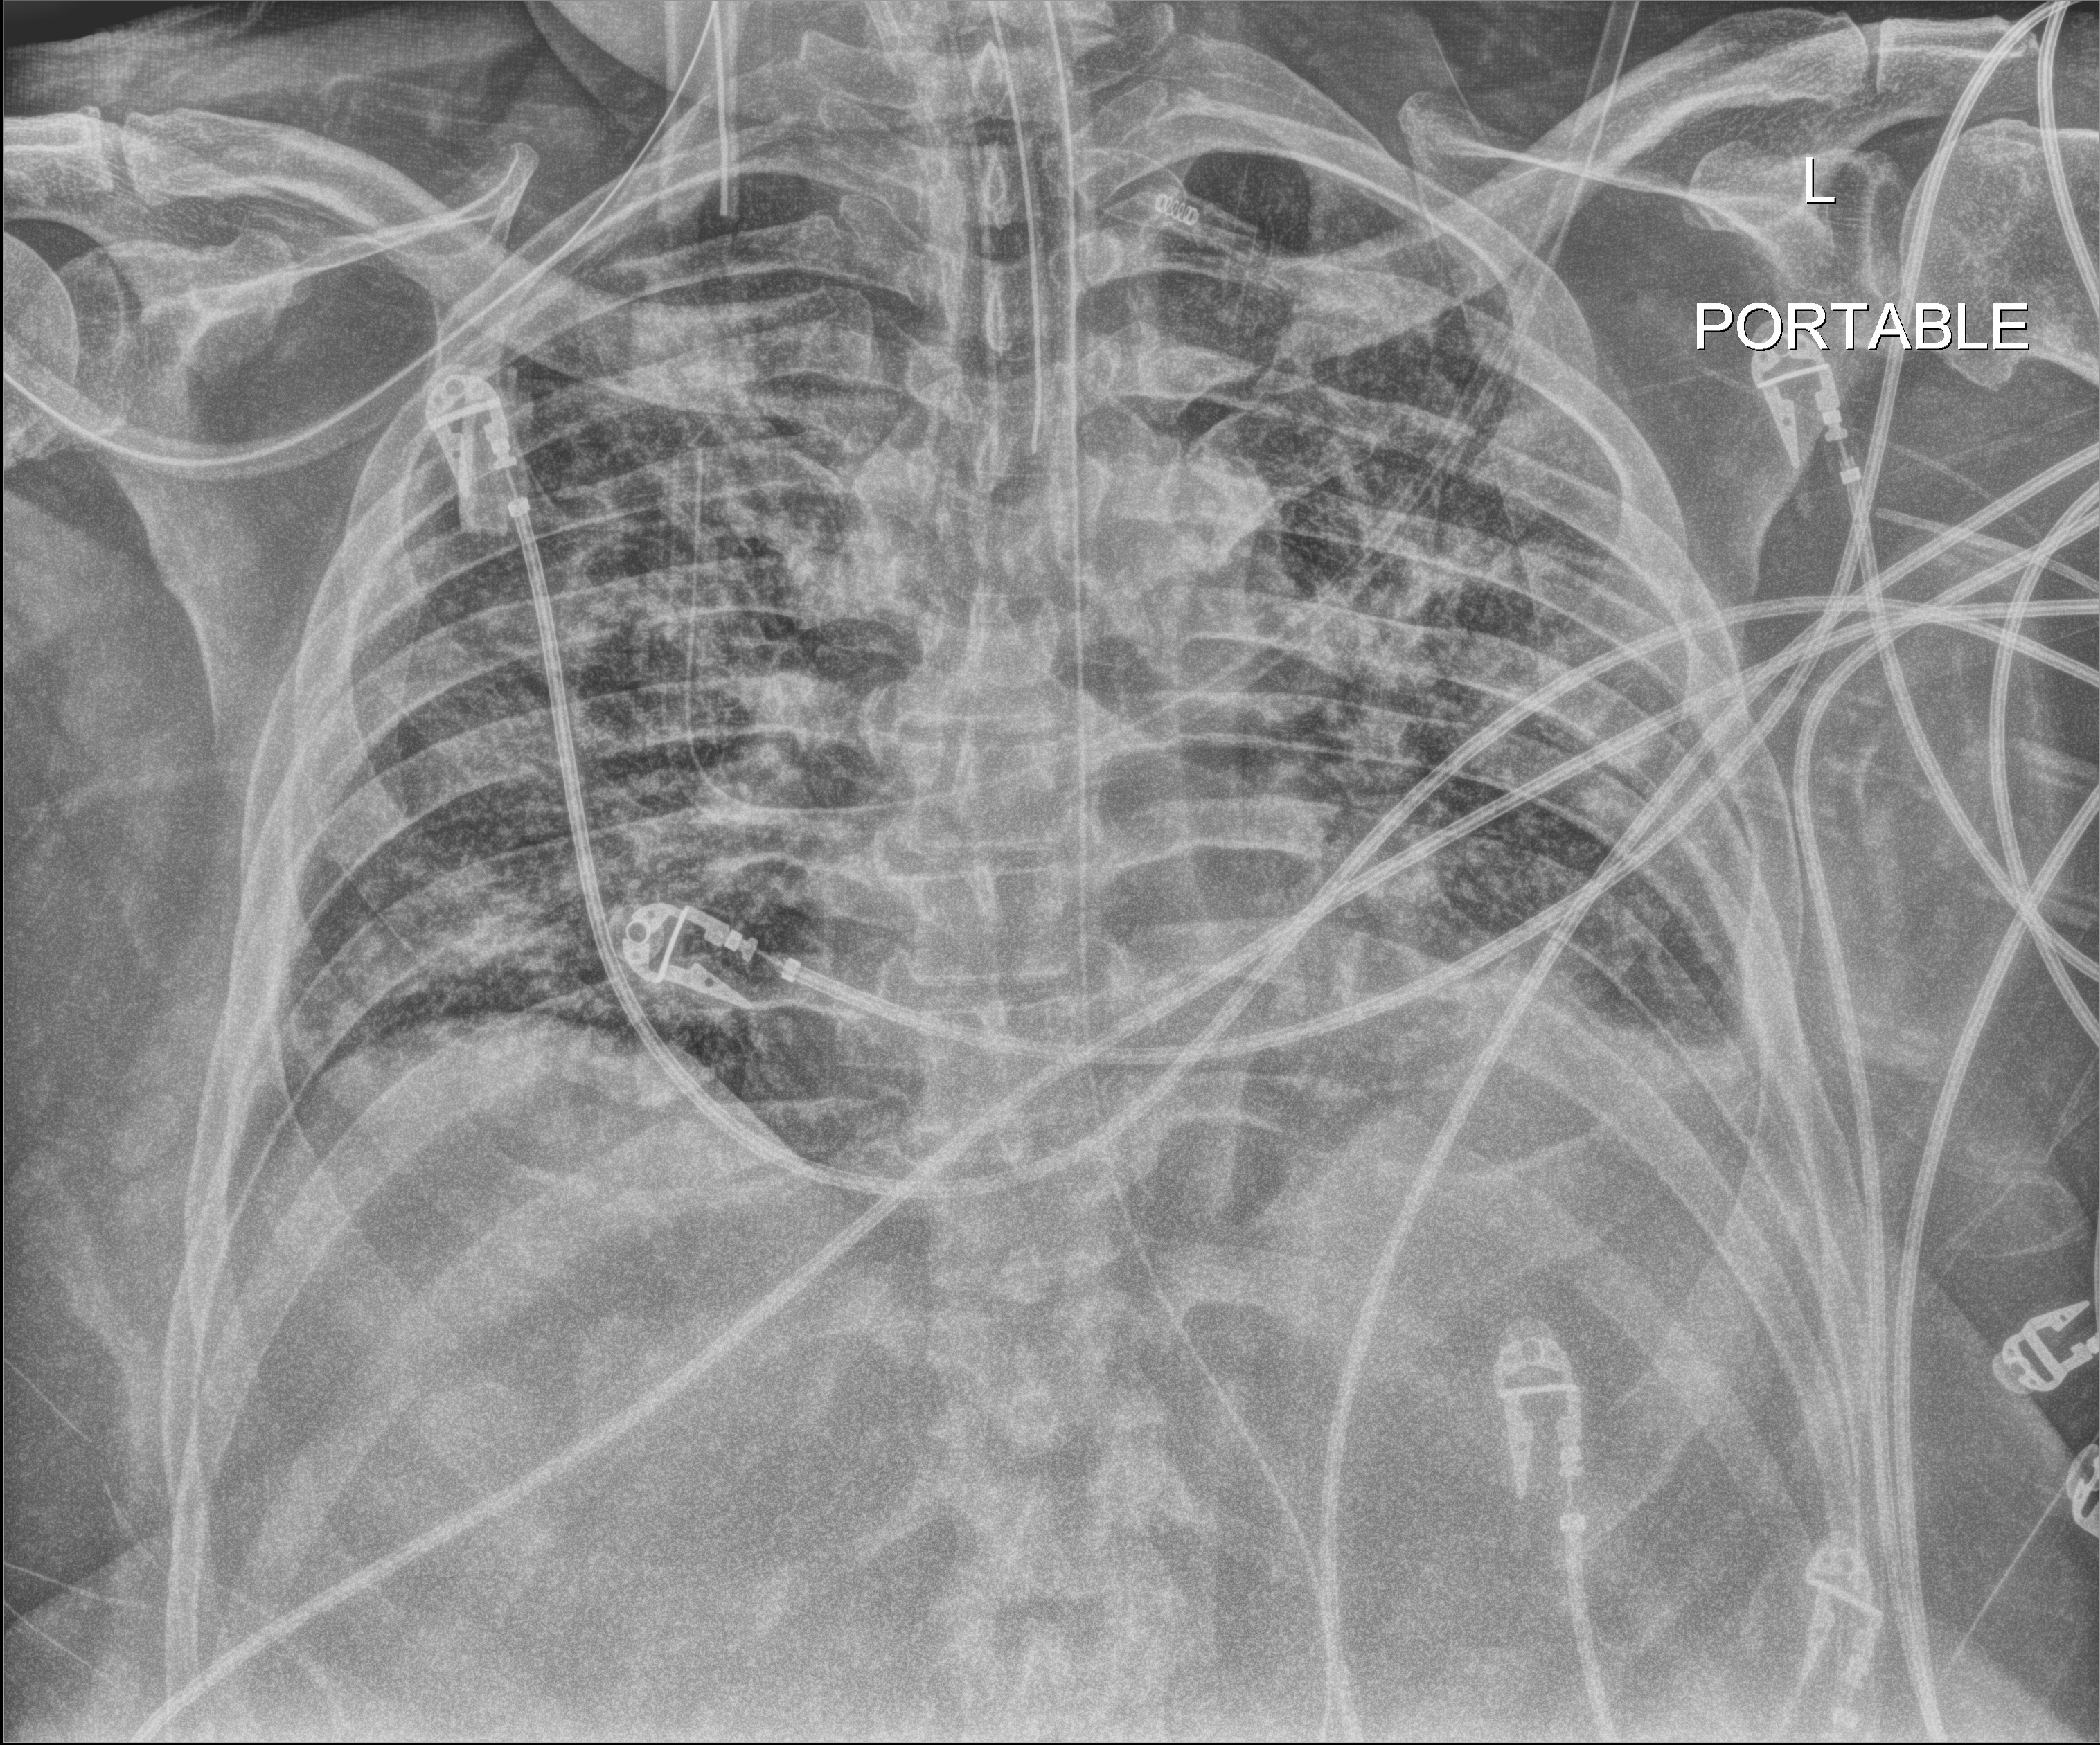
Portable chest radiograph; anteroposterior (AP) projection. Patient hospitalised with COVID-19; male, aged 18–59 years.
Admission-level facts for this patient (not findings on this image; timing relative to this image not recorded):
- diabetes (admission record): no
- COPD (admission record): no